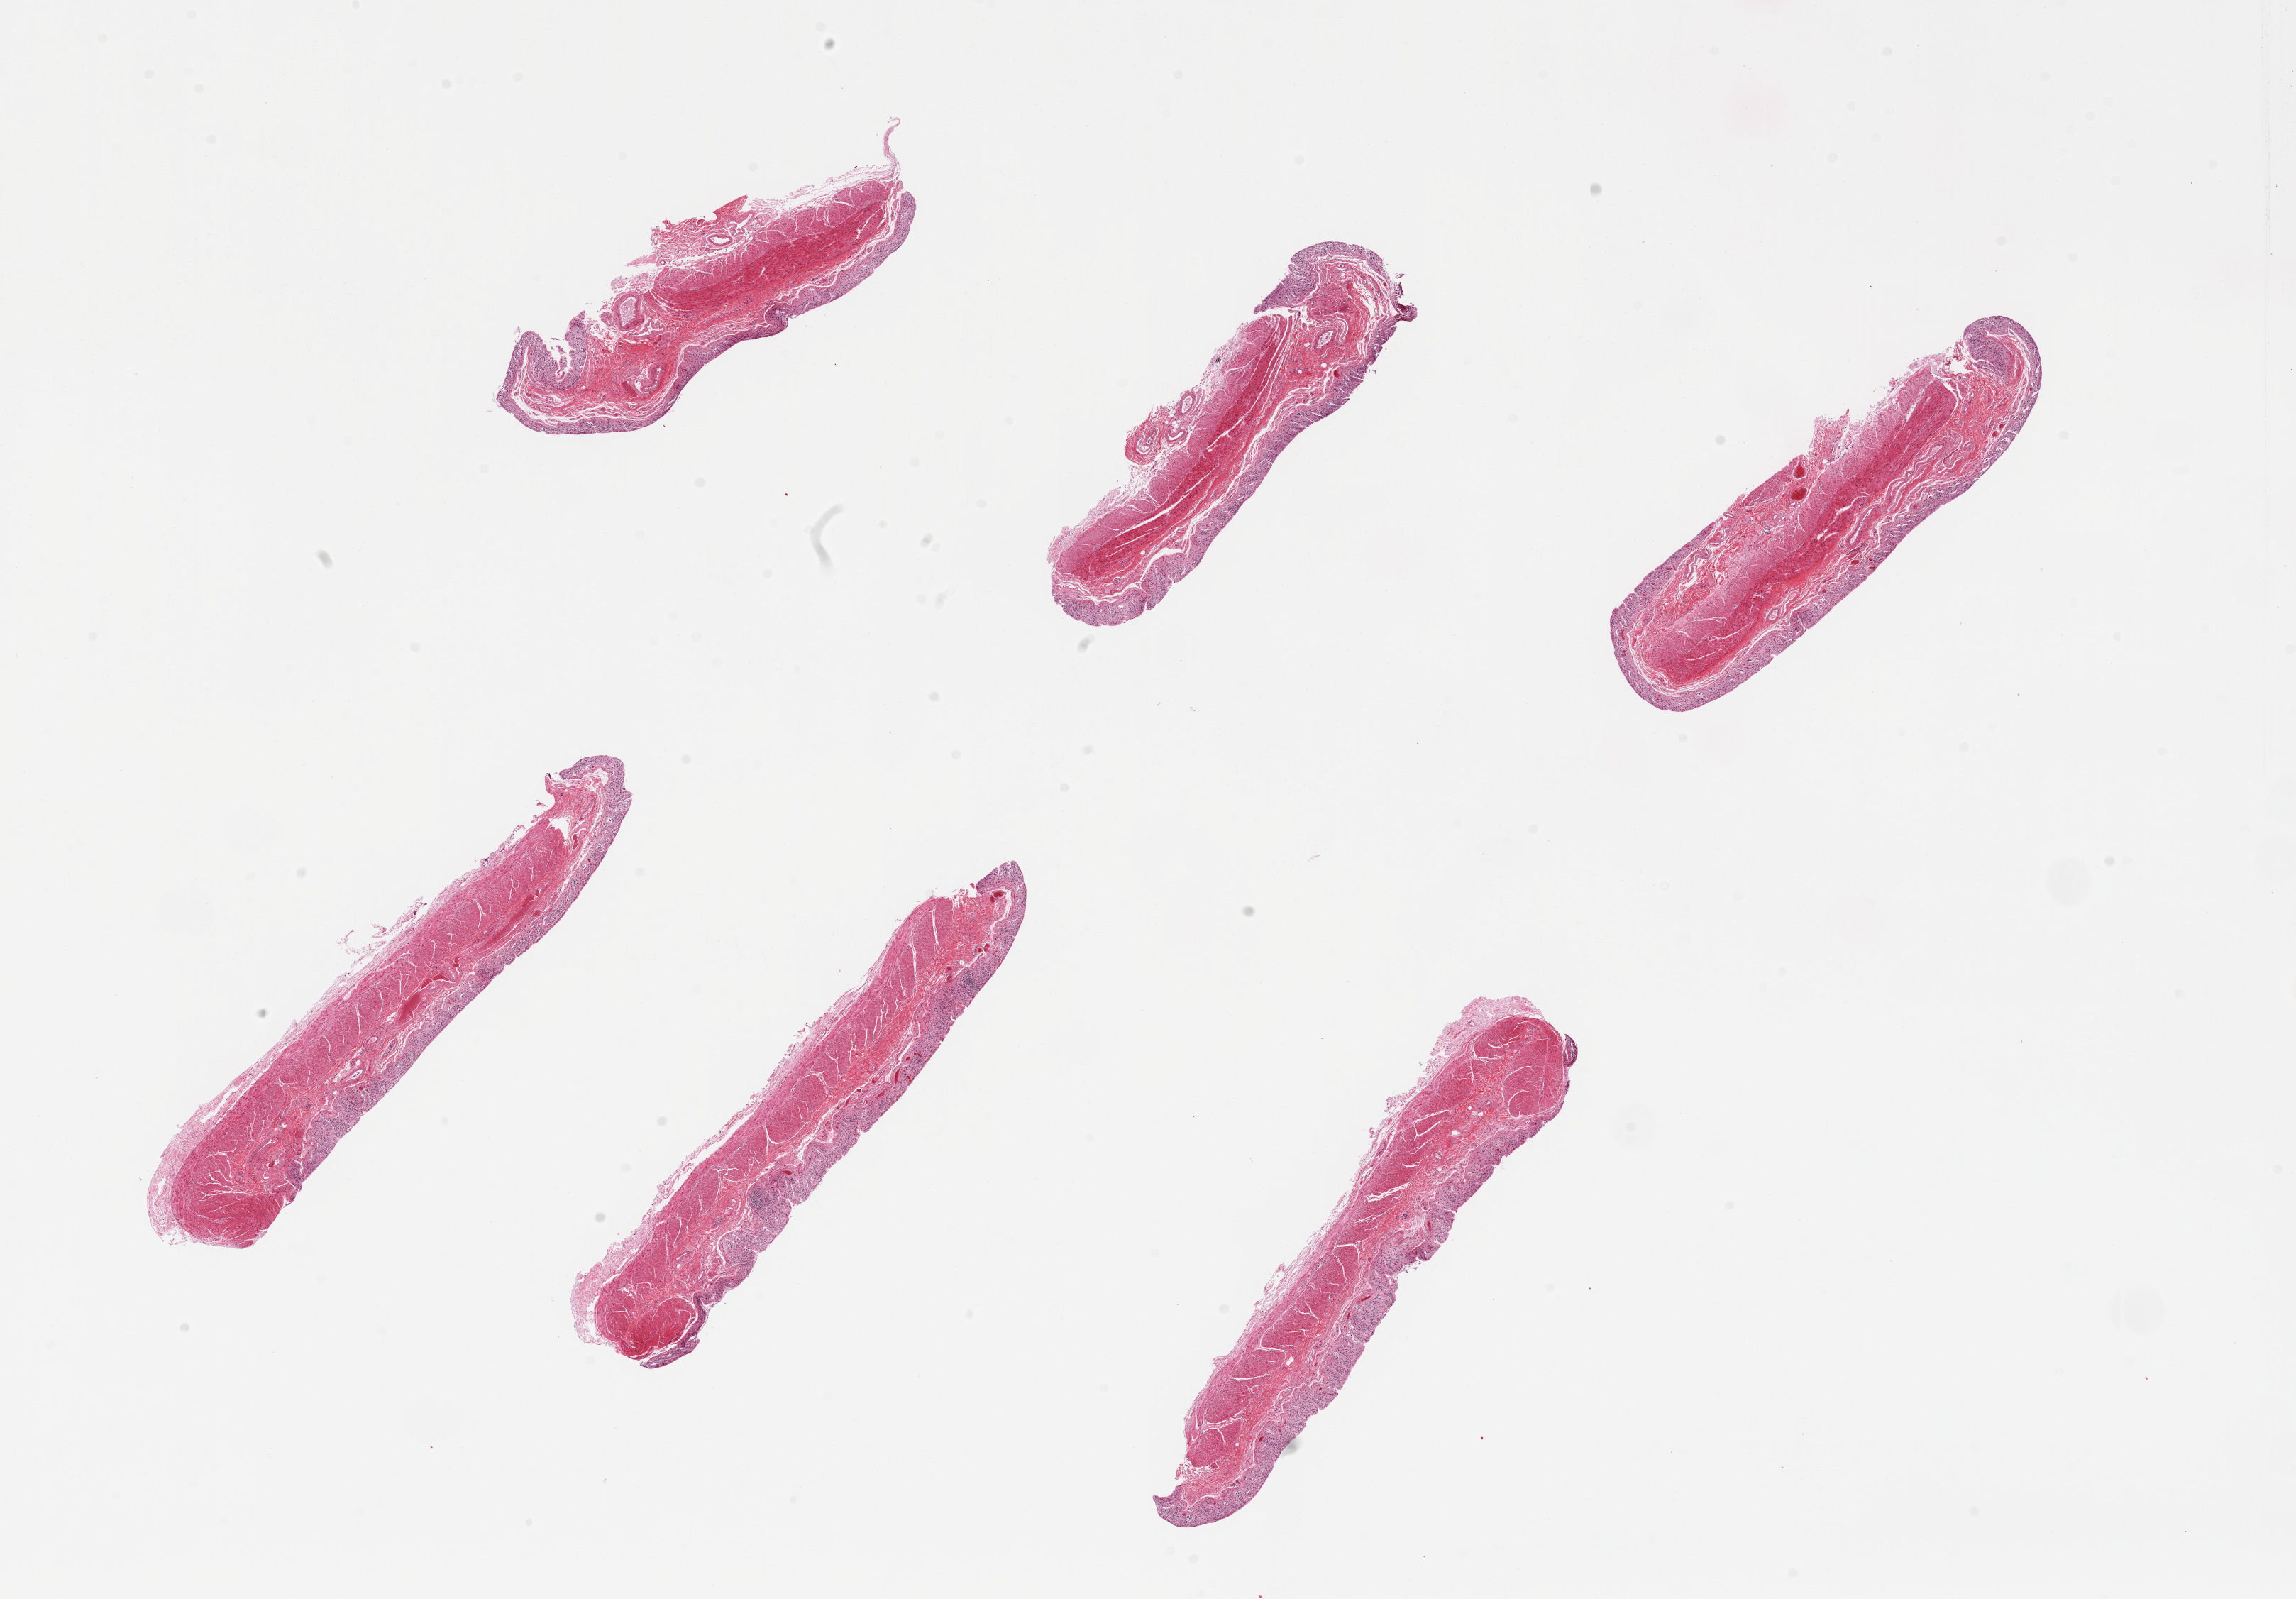
Whole-slide image, H&E stain, low-resolution overview of the scanned area, about 25.6 x 17.8 mm (slide scanned at 20x); PAXgene-fixed, paraffin-embedded tissue; target tissue: transverse colon; tissue donor sample. Female donor.
* review note (as recorded): 6 pieces; mucosa totally autolyzed; muscle slightly autolyzed